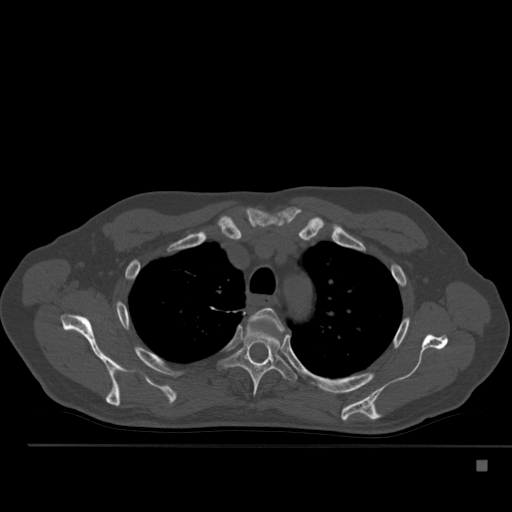
CT including the spine, one axial slice. Slice 385 of 517 in the series (ordered by position). 120 kVp. Bone window (W 1800 / L 400 HU). 1.5 mm slice thickness. 512 × 512 image matrix. Patient: male, 70 years. From the clinical record (not read from this slice): primary cancer: renal; vertebrae with lytic lesions (as recorded): T4, T6, T10, T12, L3, L4, L5.
Annotated regions visible in this slice (semi-automatic segmentation, software-assisted and operator-edited):
- T3 vertebra: bounding box [x1, y1, x2, y2] px = [249, 307, 285, 331]
- T4 vertebra: [218, 323, 297, 396]